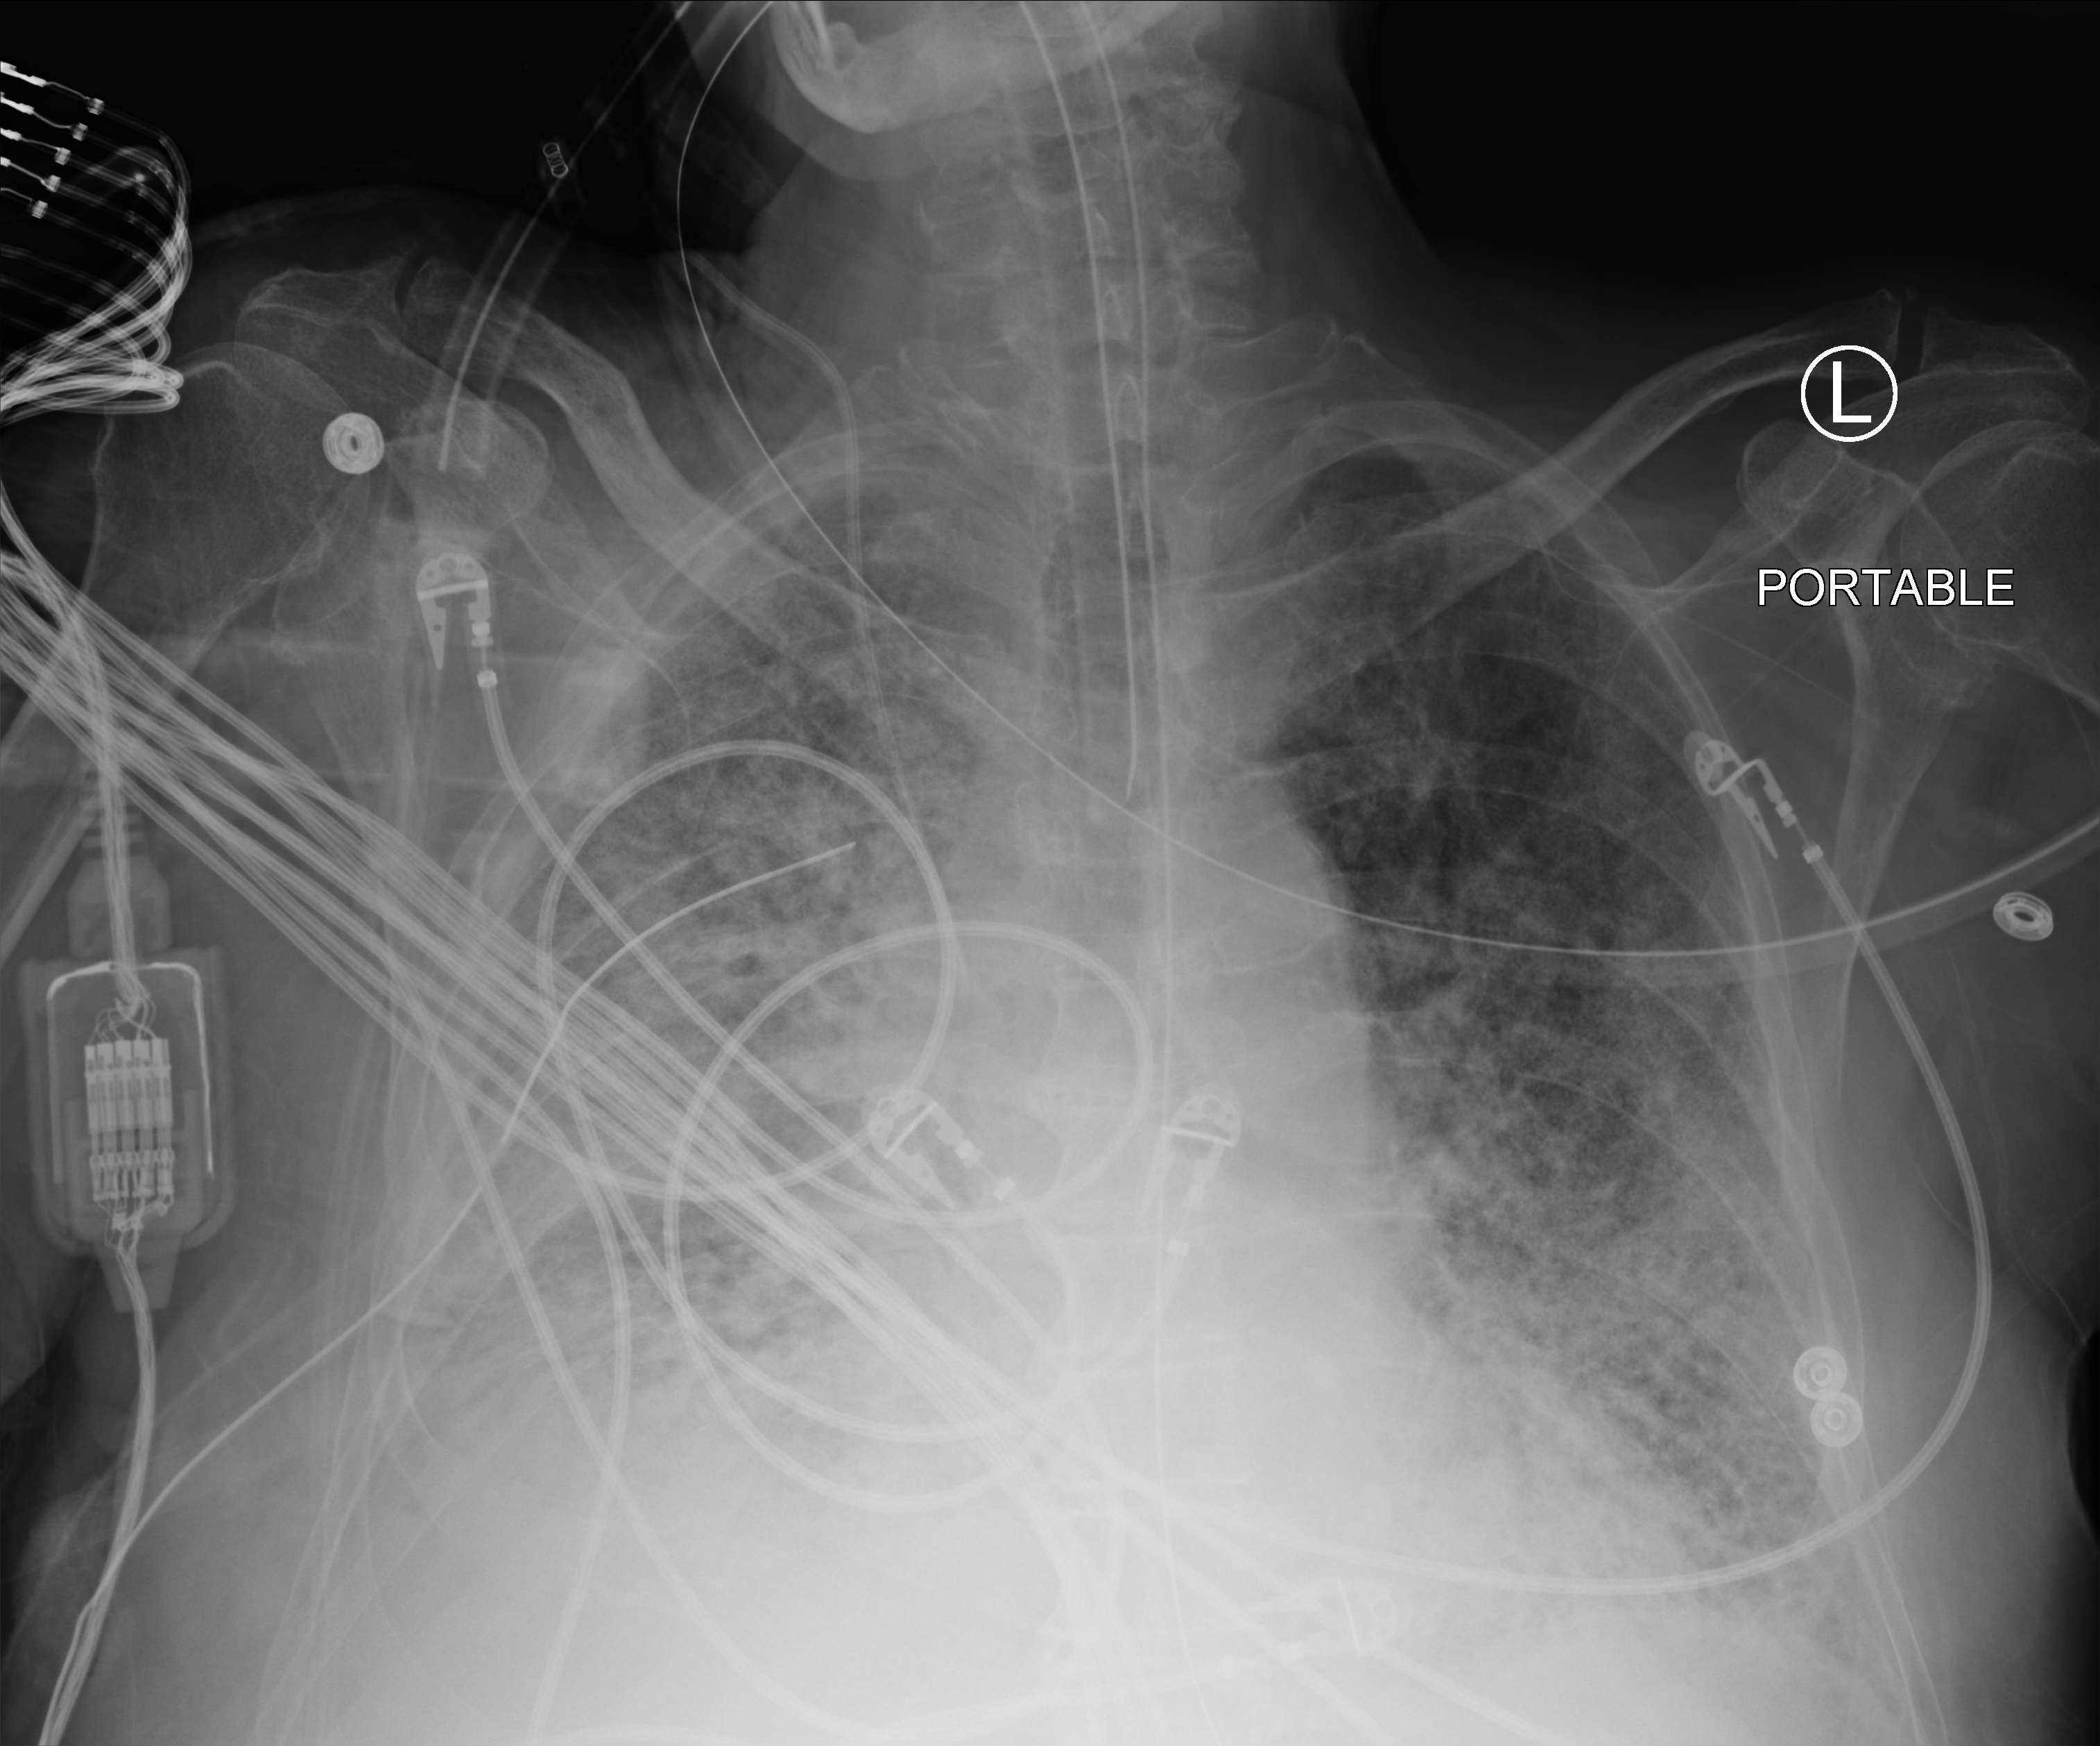
Chest X-ray (portable); anteroposterior (AP) projection. Male patient hospitalised with COVID-19, age 75–90 years.
Admission-level facts for this patient (not findings on this image; timing relative to this image not recorded): admitted to intensive care during this hospital stay: yes.